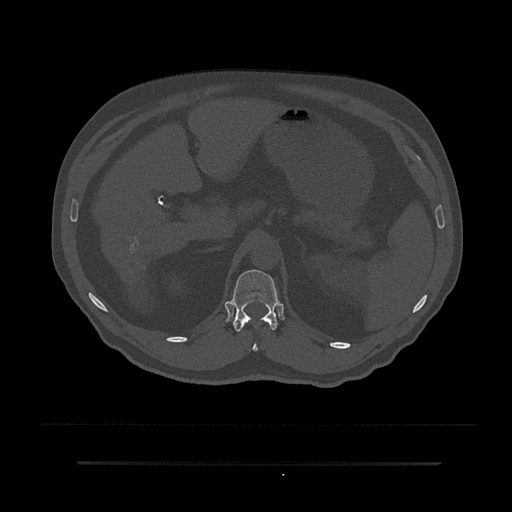
CT including the spine, one axial slice. Slice 218 of 797 in the series (ordered by position). Reconstruction kernel Br40s/3. 120 kVp. Bone window (W 1800 / L 400 HU). 512 × 512 image matrix, field of view 464 × 464 mm. Patient: male, 59 years. From the clinical record (not read from this slice): primary cancer: bile ducts; vertebrae with lytic lesions (as recorded): T10.
Annotated regions visible in this slice (semi-automatically segmented with operator editing):
- T12 vertebra: box from (x=229, y=269) to (x=279, y=351) px